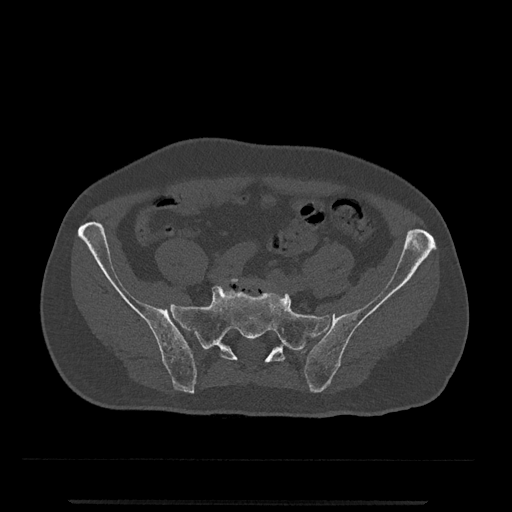
CT including the spine, one axial slice. Slice 12 of 797 in the series (ordered by position). Reconstruction kernel Br40s/3. 120 kVp. Bone window (W 1800 / L 400 HU). 0.5 mm slice thickness. 512 × 512 image matrix, field of view 419 × 419 mm. Male patient, age 63 years. Case-level facts recorded for this patient, not image findings: primary cancer: prostate.
Outlined on this slice (semi-automatic segmentation, software-assisted and operator-edited):
- L5 vertebra: box from (x=228, y=278) to (x=267, y=286) px